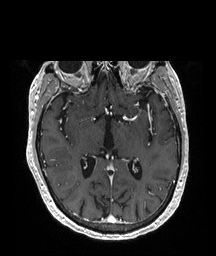
Brain MRI from a brain-tumour surgery series, one axial slice. Slice 114 of 208 in the series (ordered by position). T1-weighted post-contrast. 1 mm slice thickness. 216 × 256 image matrix, field of view 216 × 256 mm. Case-level facts recorded for this patient, not image findings: histopathology: Glioblastoma; WHO grade: 4; IDH mutation: no.
Outlined on this slice (manually delineated by an expert):
- tumour: bounding box <59,179,76,190> (left, top, right, bottom; pixels)